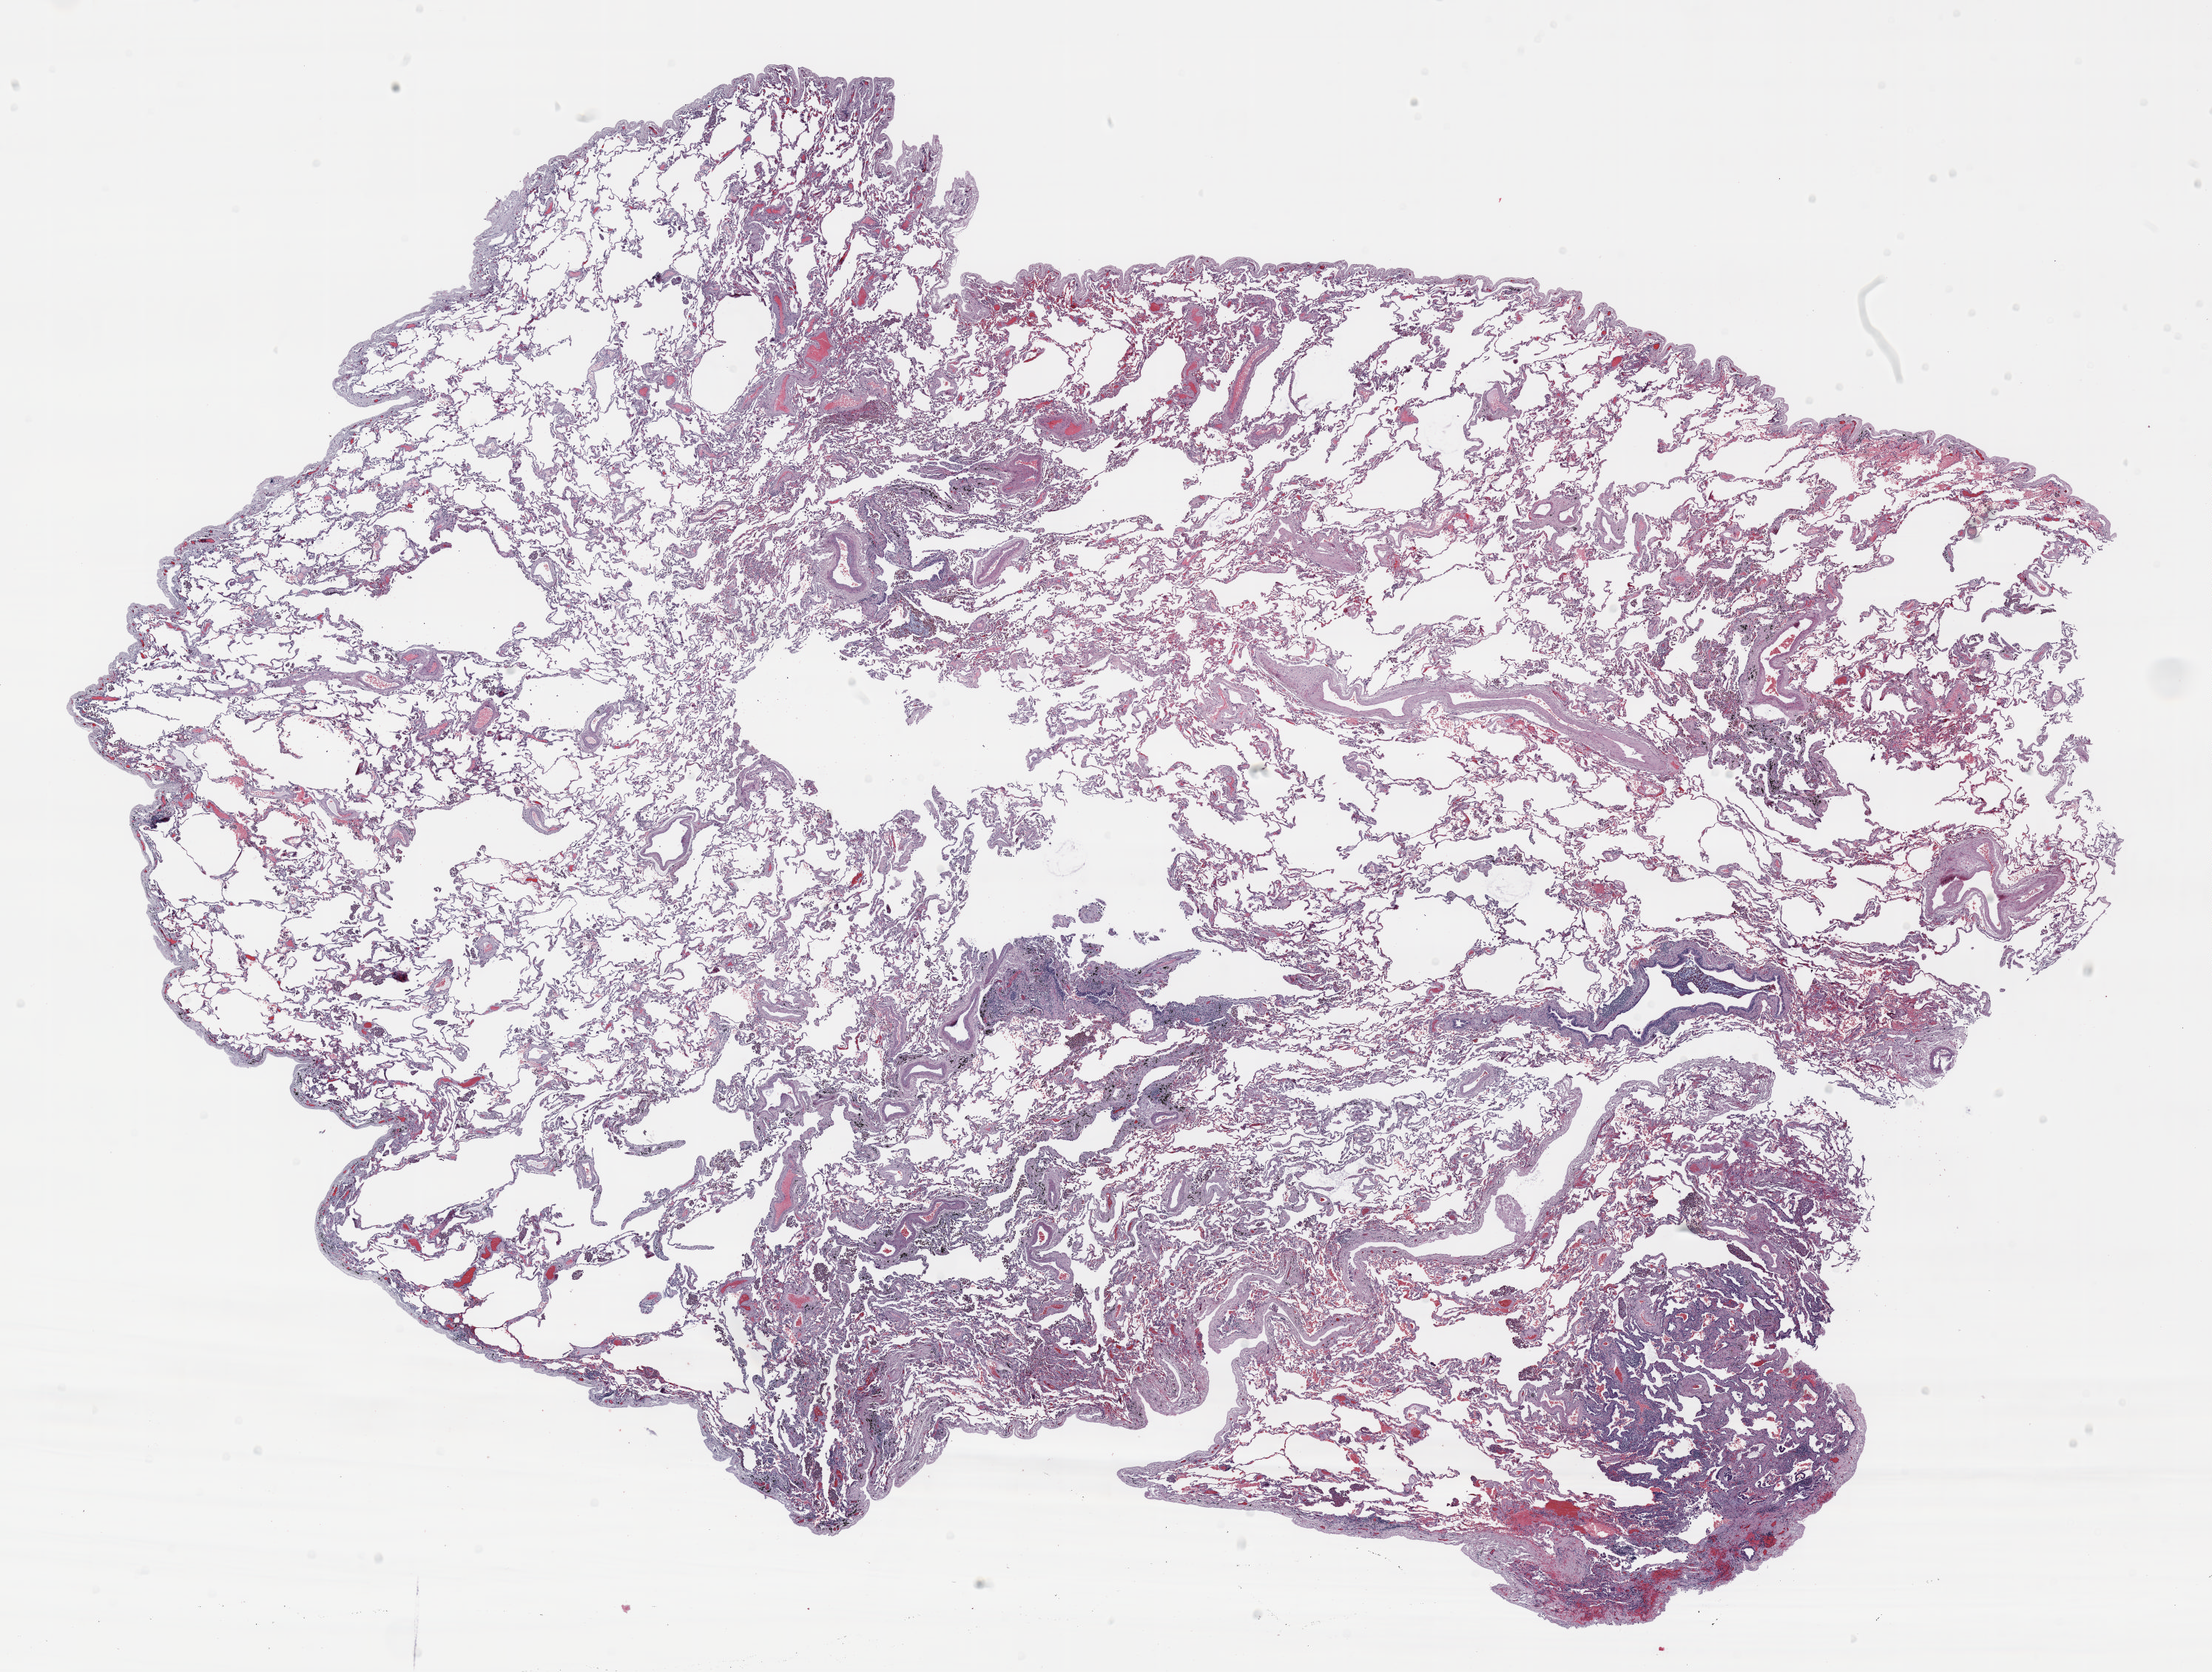
Whole-slide histology image, H&E, whole scanned area (about 24.0 x 18.2 mm) shown as a low-resolution overview; FFPE section; lung. Male patient, aged 73 at enrolment. Grade: well differentiated (G1).
- stage (AJCC 6th edition): IA
- tumour size (pathology): 11 mm
- primary tumour location (clinical record): right middle lobe
- participant's lung-cancer diagnosis: Bronchiolo-alveolar adenocarcinoma, NOS